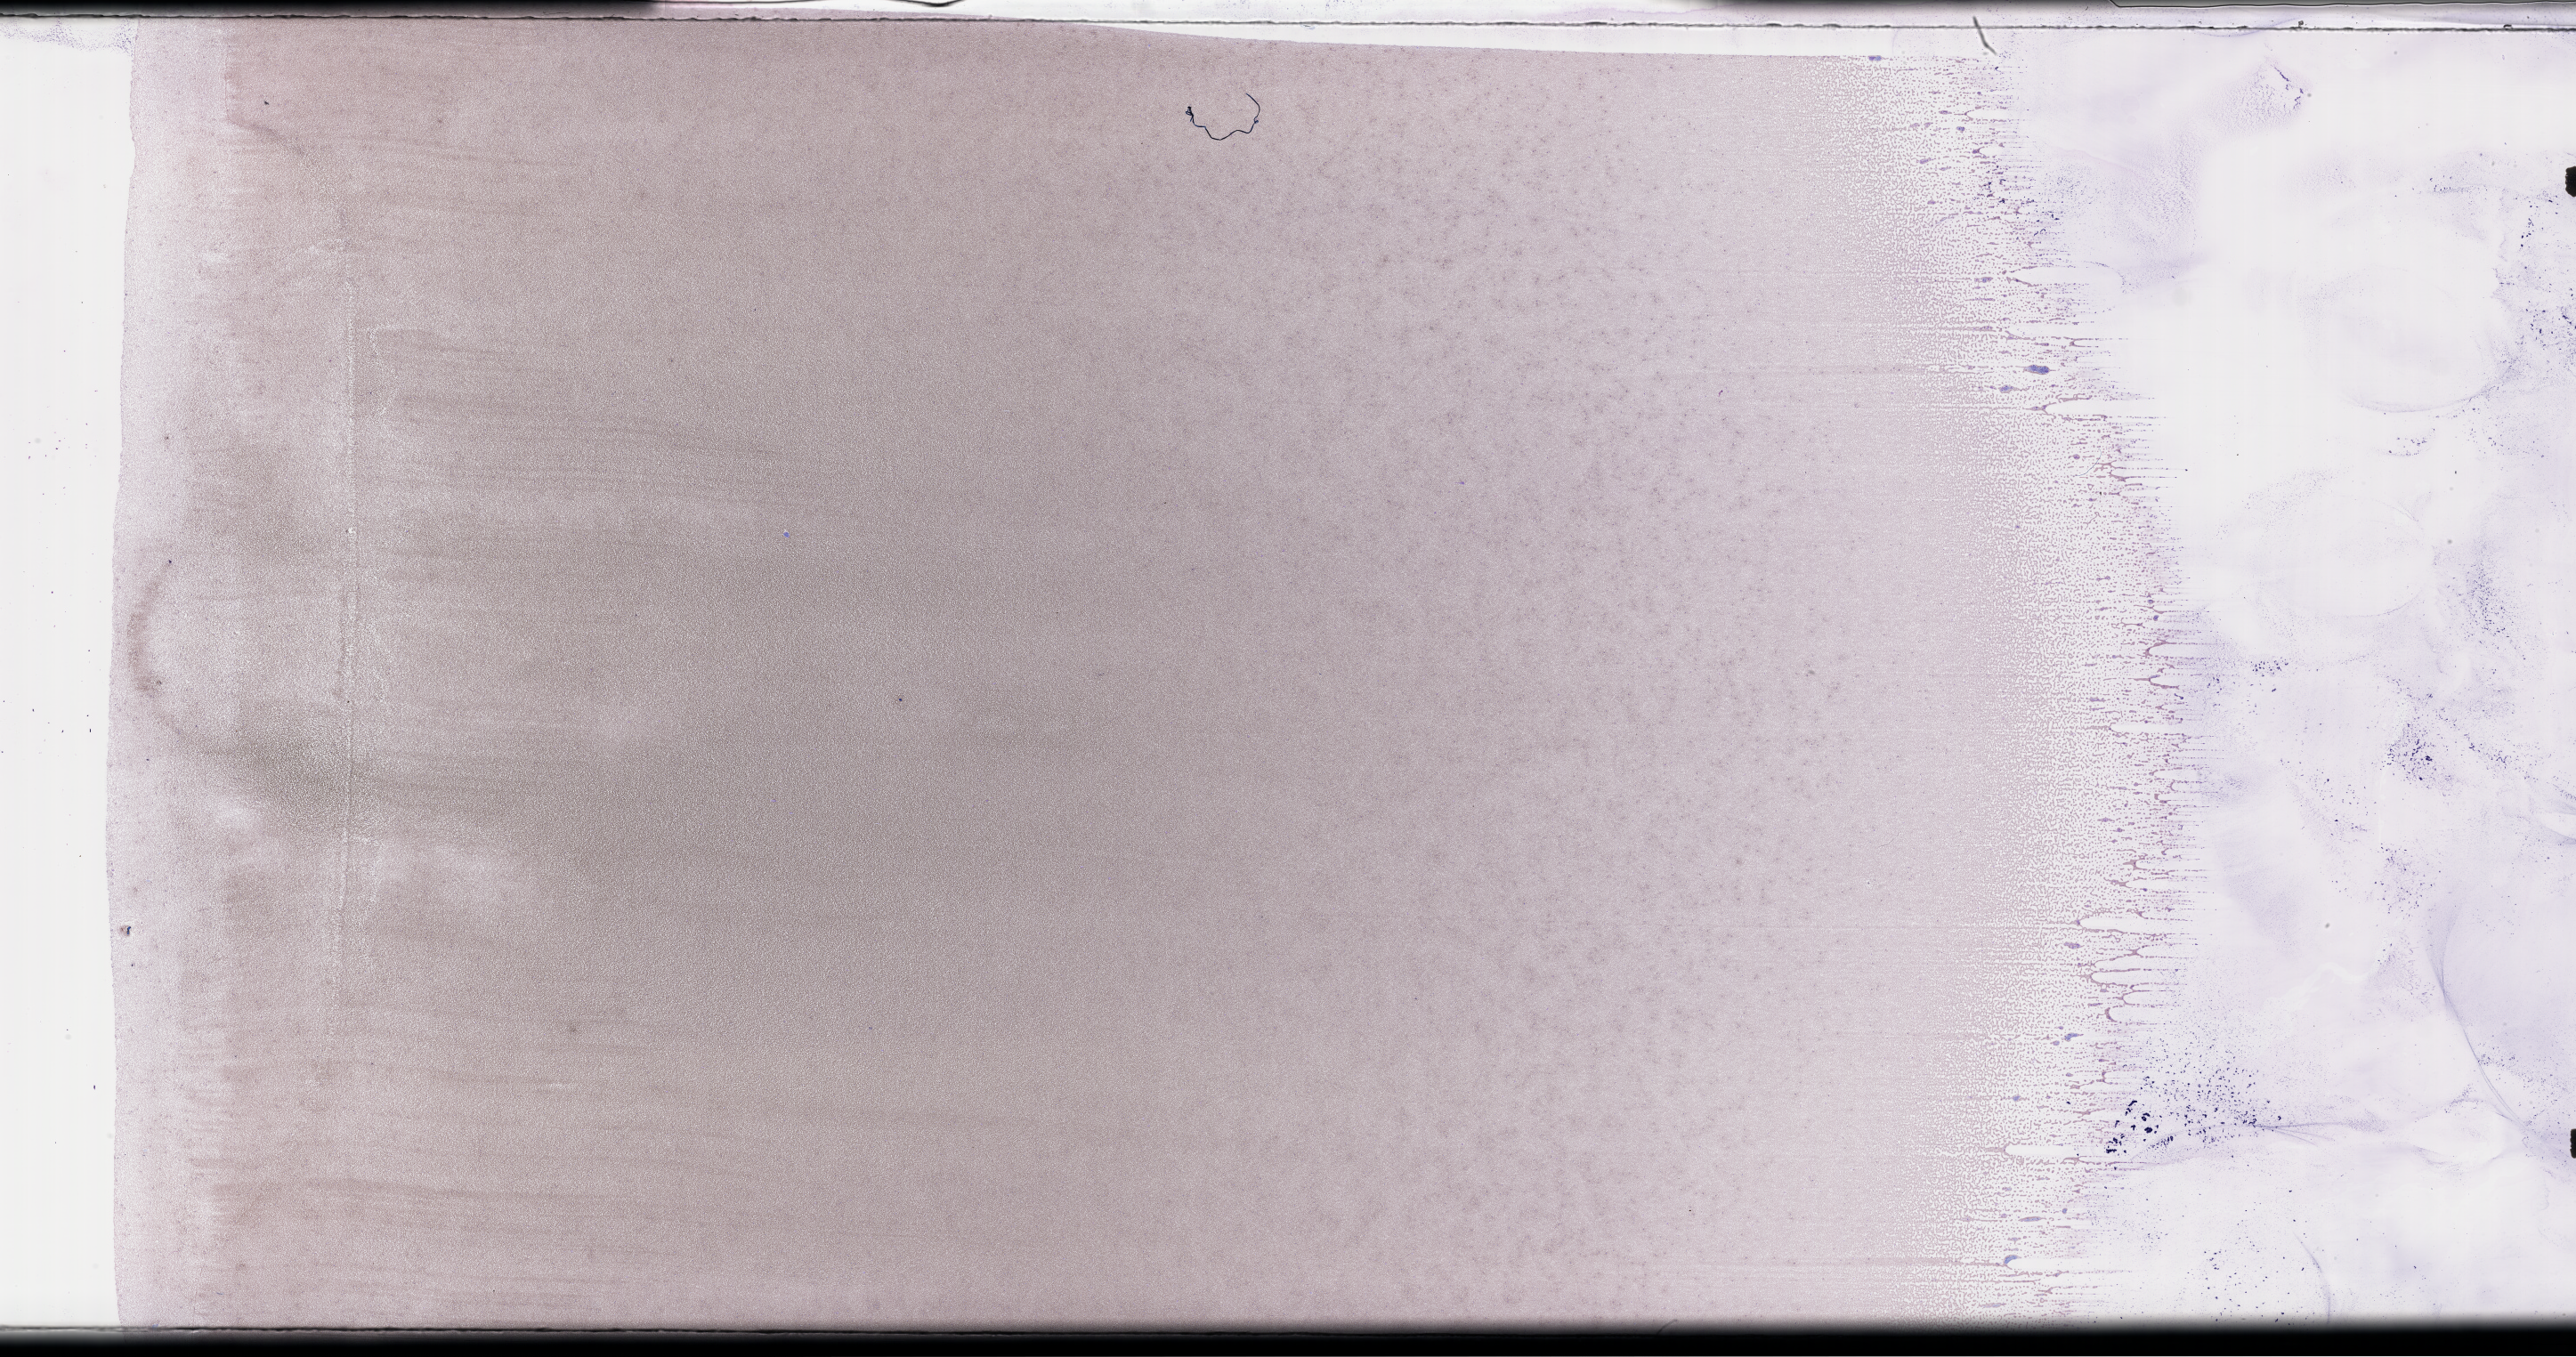
Wright-Giemsa-stained whole blood smear, whole-slide image — low-resolution overview of the scanned area, about 46.7 x 24.6 mm, collected on treatment. Patient sex: male.
Patient diagnosis: Plasma Cell Myeloma.